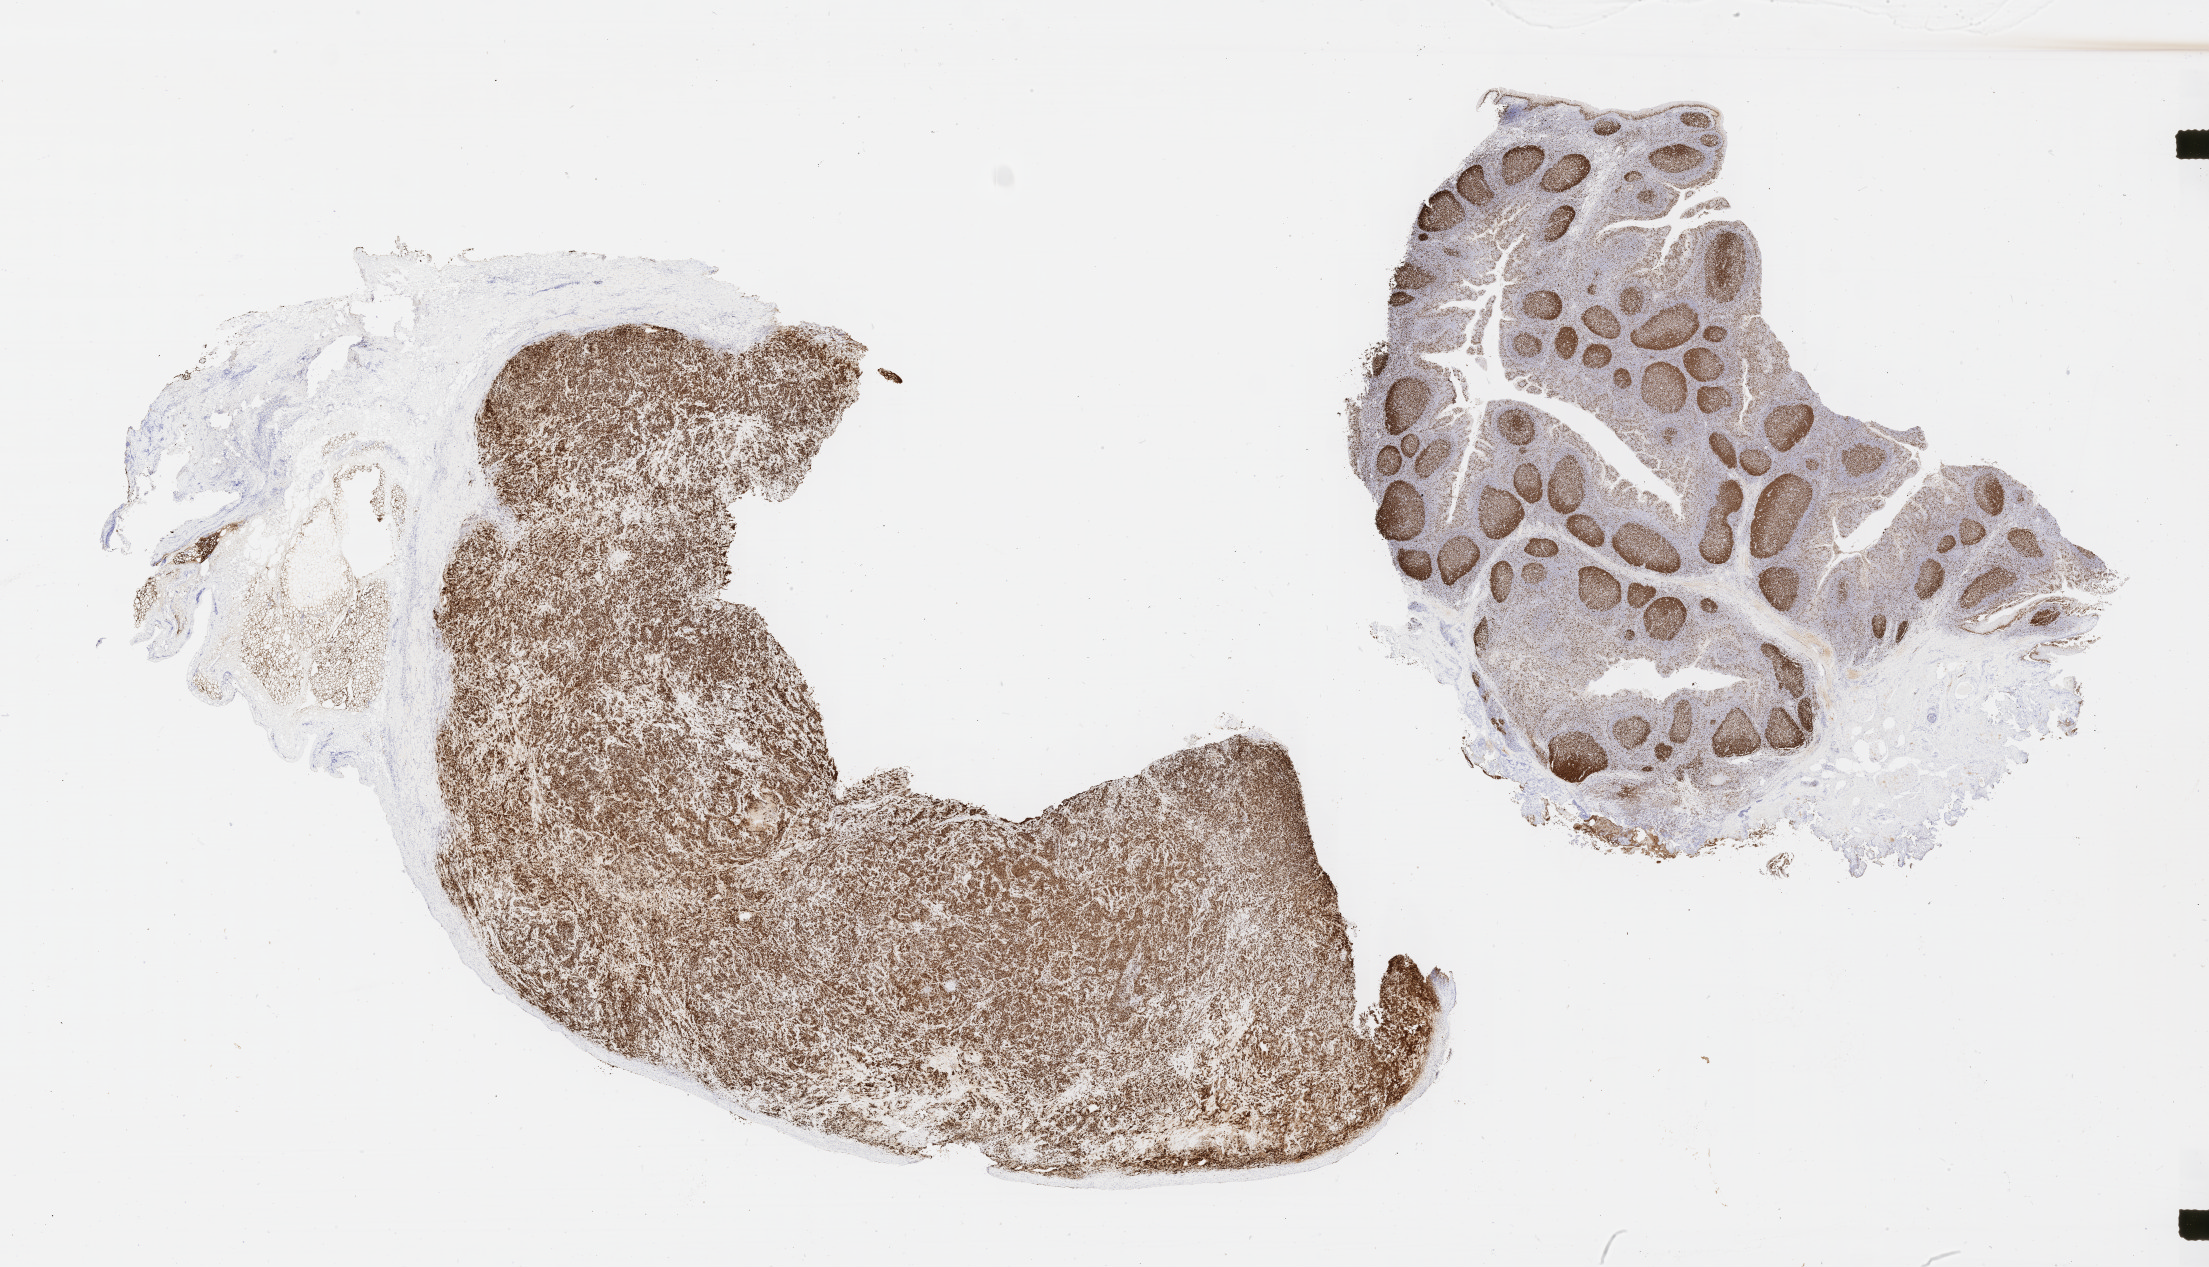
IHC for Ki-67, whole-slide image, a low-resolution overview of the entire scanned area, about 35.7 x 20.5 mm; specimen: tumor tissue; anatomic site: bone. Patient male; 48 years old.
Histologic diagnosis: Diffuse large B-cell lymphoma, NOS.